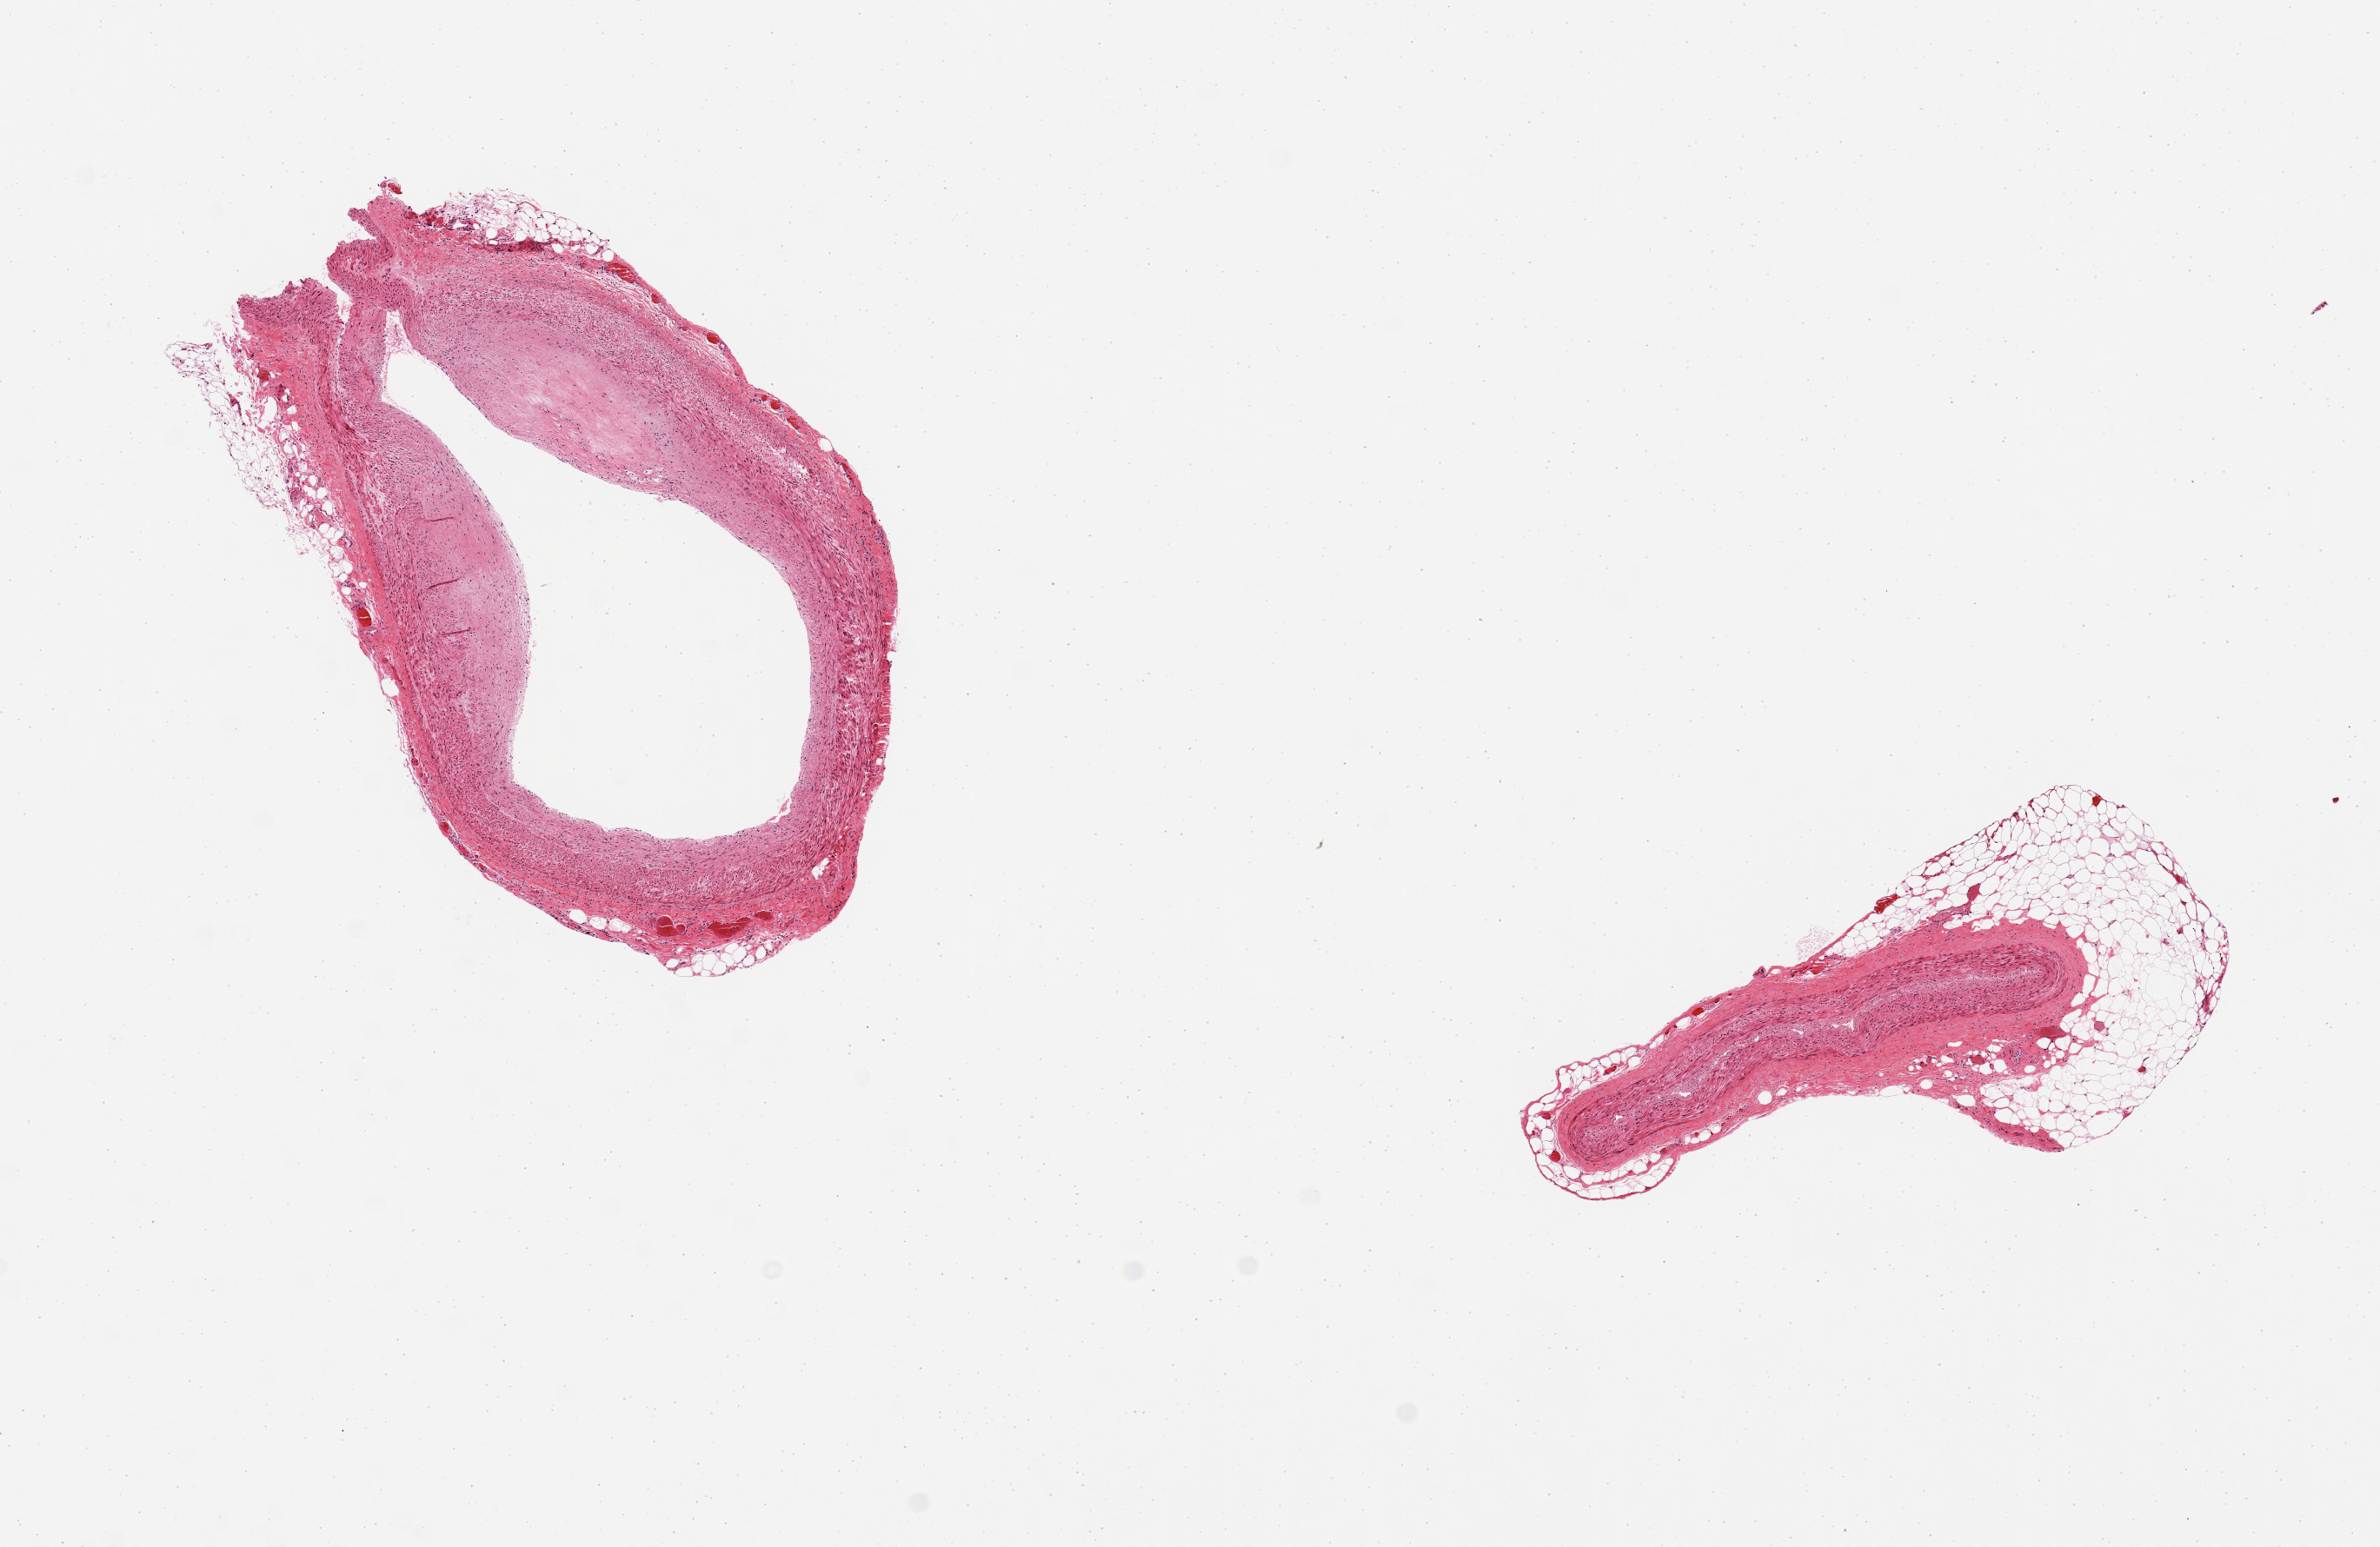
Digitized H&E-stained section — a low-resolution overview of the entire scanned area, about 10.8 x 7.0 mm; PAXgene-fixed paraffin-embedded (PFPE) section; section of coronary artery (target tissue); donor tissue sample. Donor: male.
Pathologist's review note for this sample: 2 pieces; 1 has 1 x 0.5 mm plaque; other (smaller) has 40% external fat.